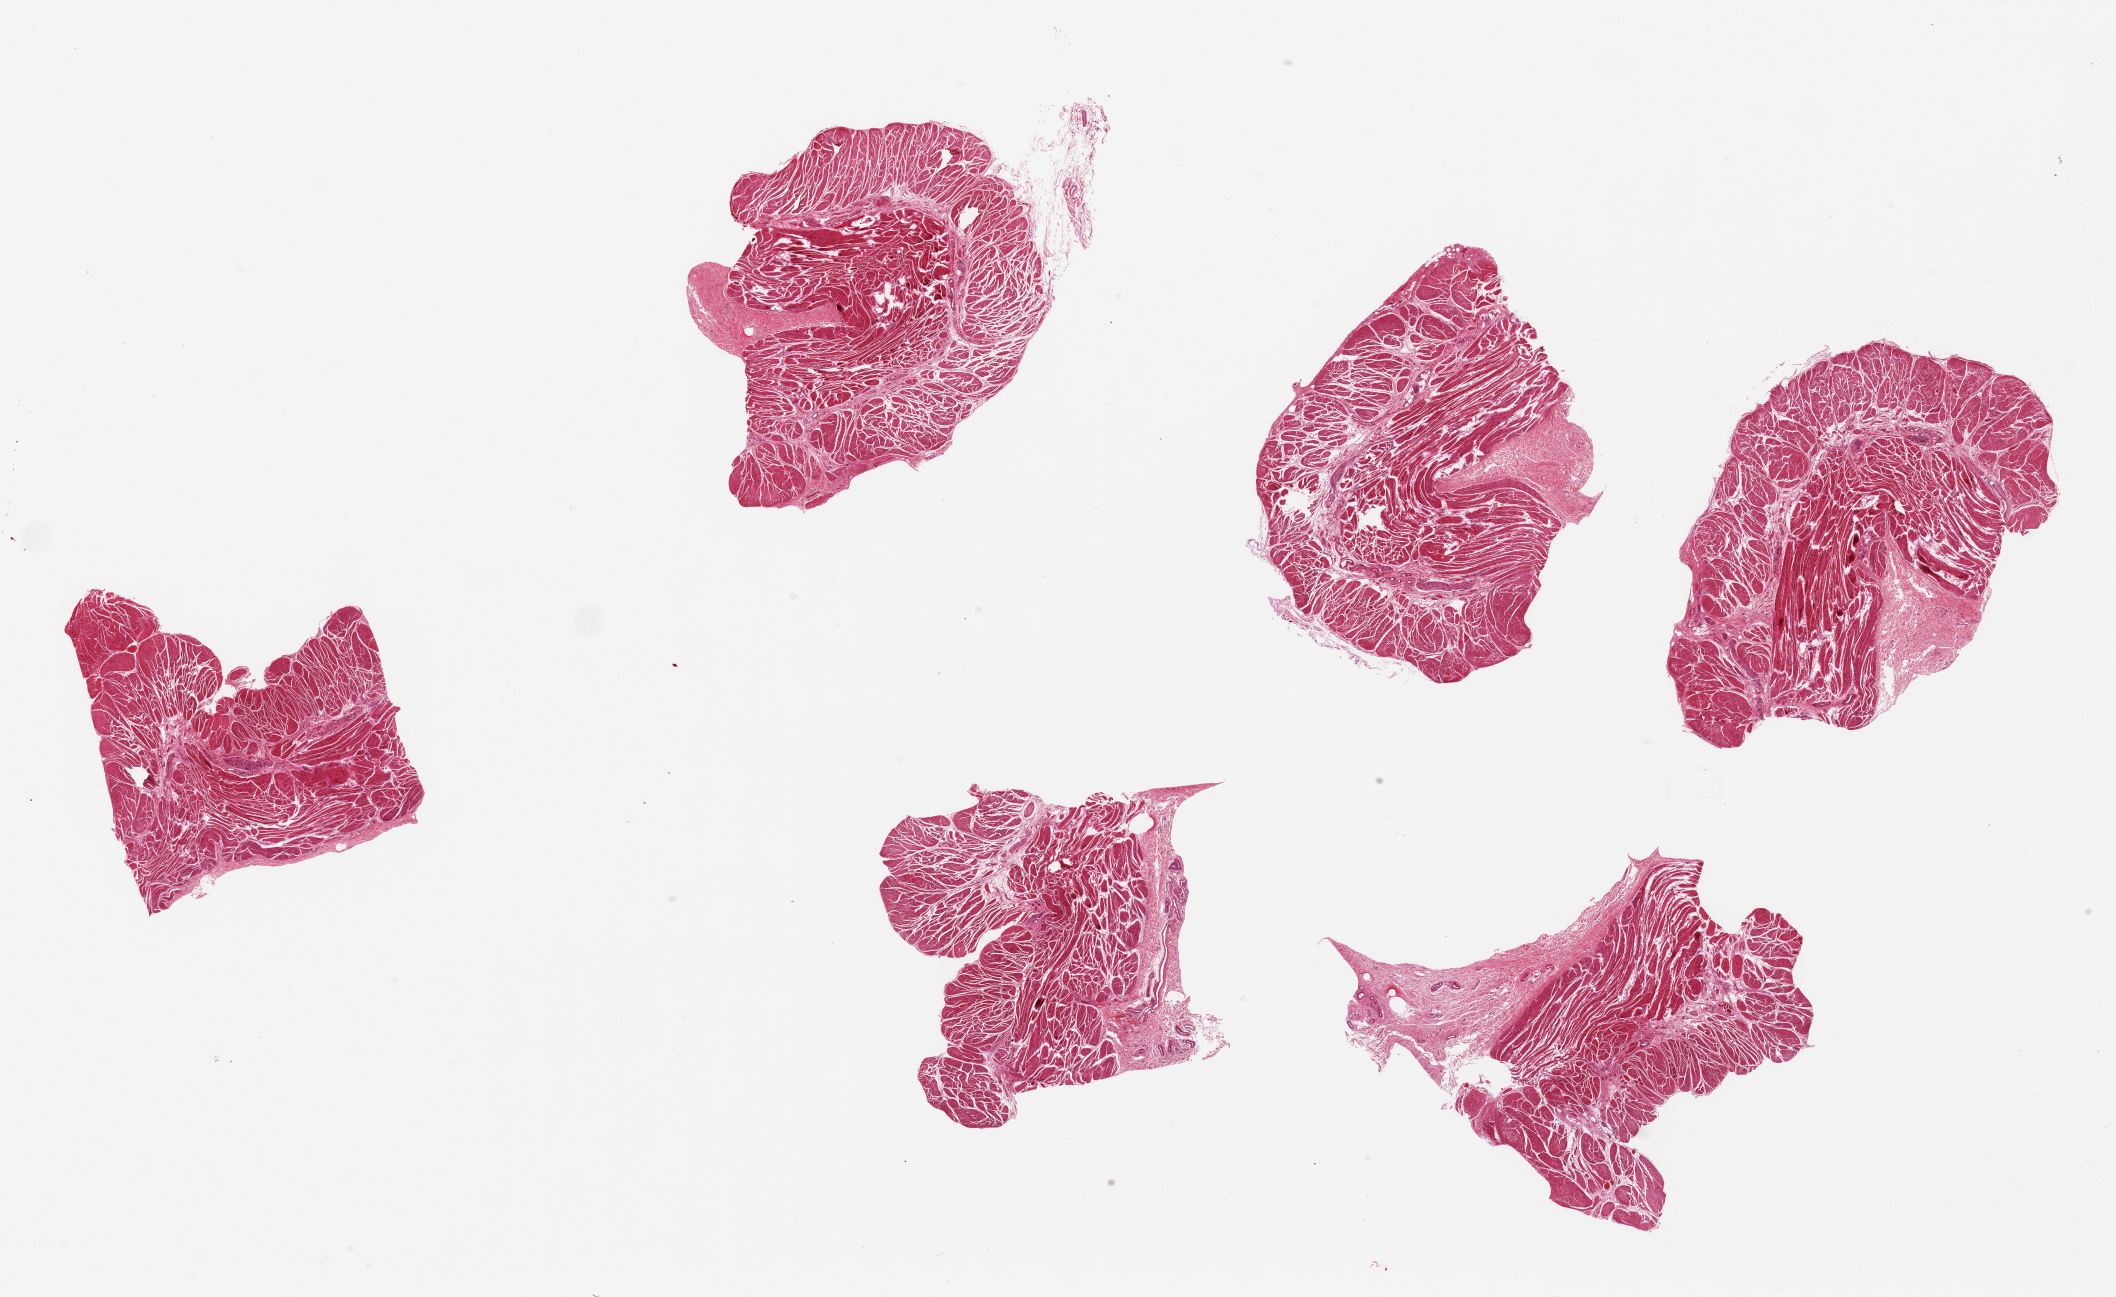
H&E whole-slide image, brightfield — whole scanned area (about 33.5 x 20.5 mm, from a 20x scan) shown as a low-resolution overview, PAXgene-fixed, paraffin-embedded tissue, sampled site (target tissue): esophageal muscle, tissue donor sample. Donor: female.
Review note (as recorded): 6 pieces ~7x5mm.